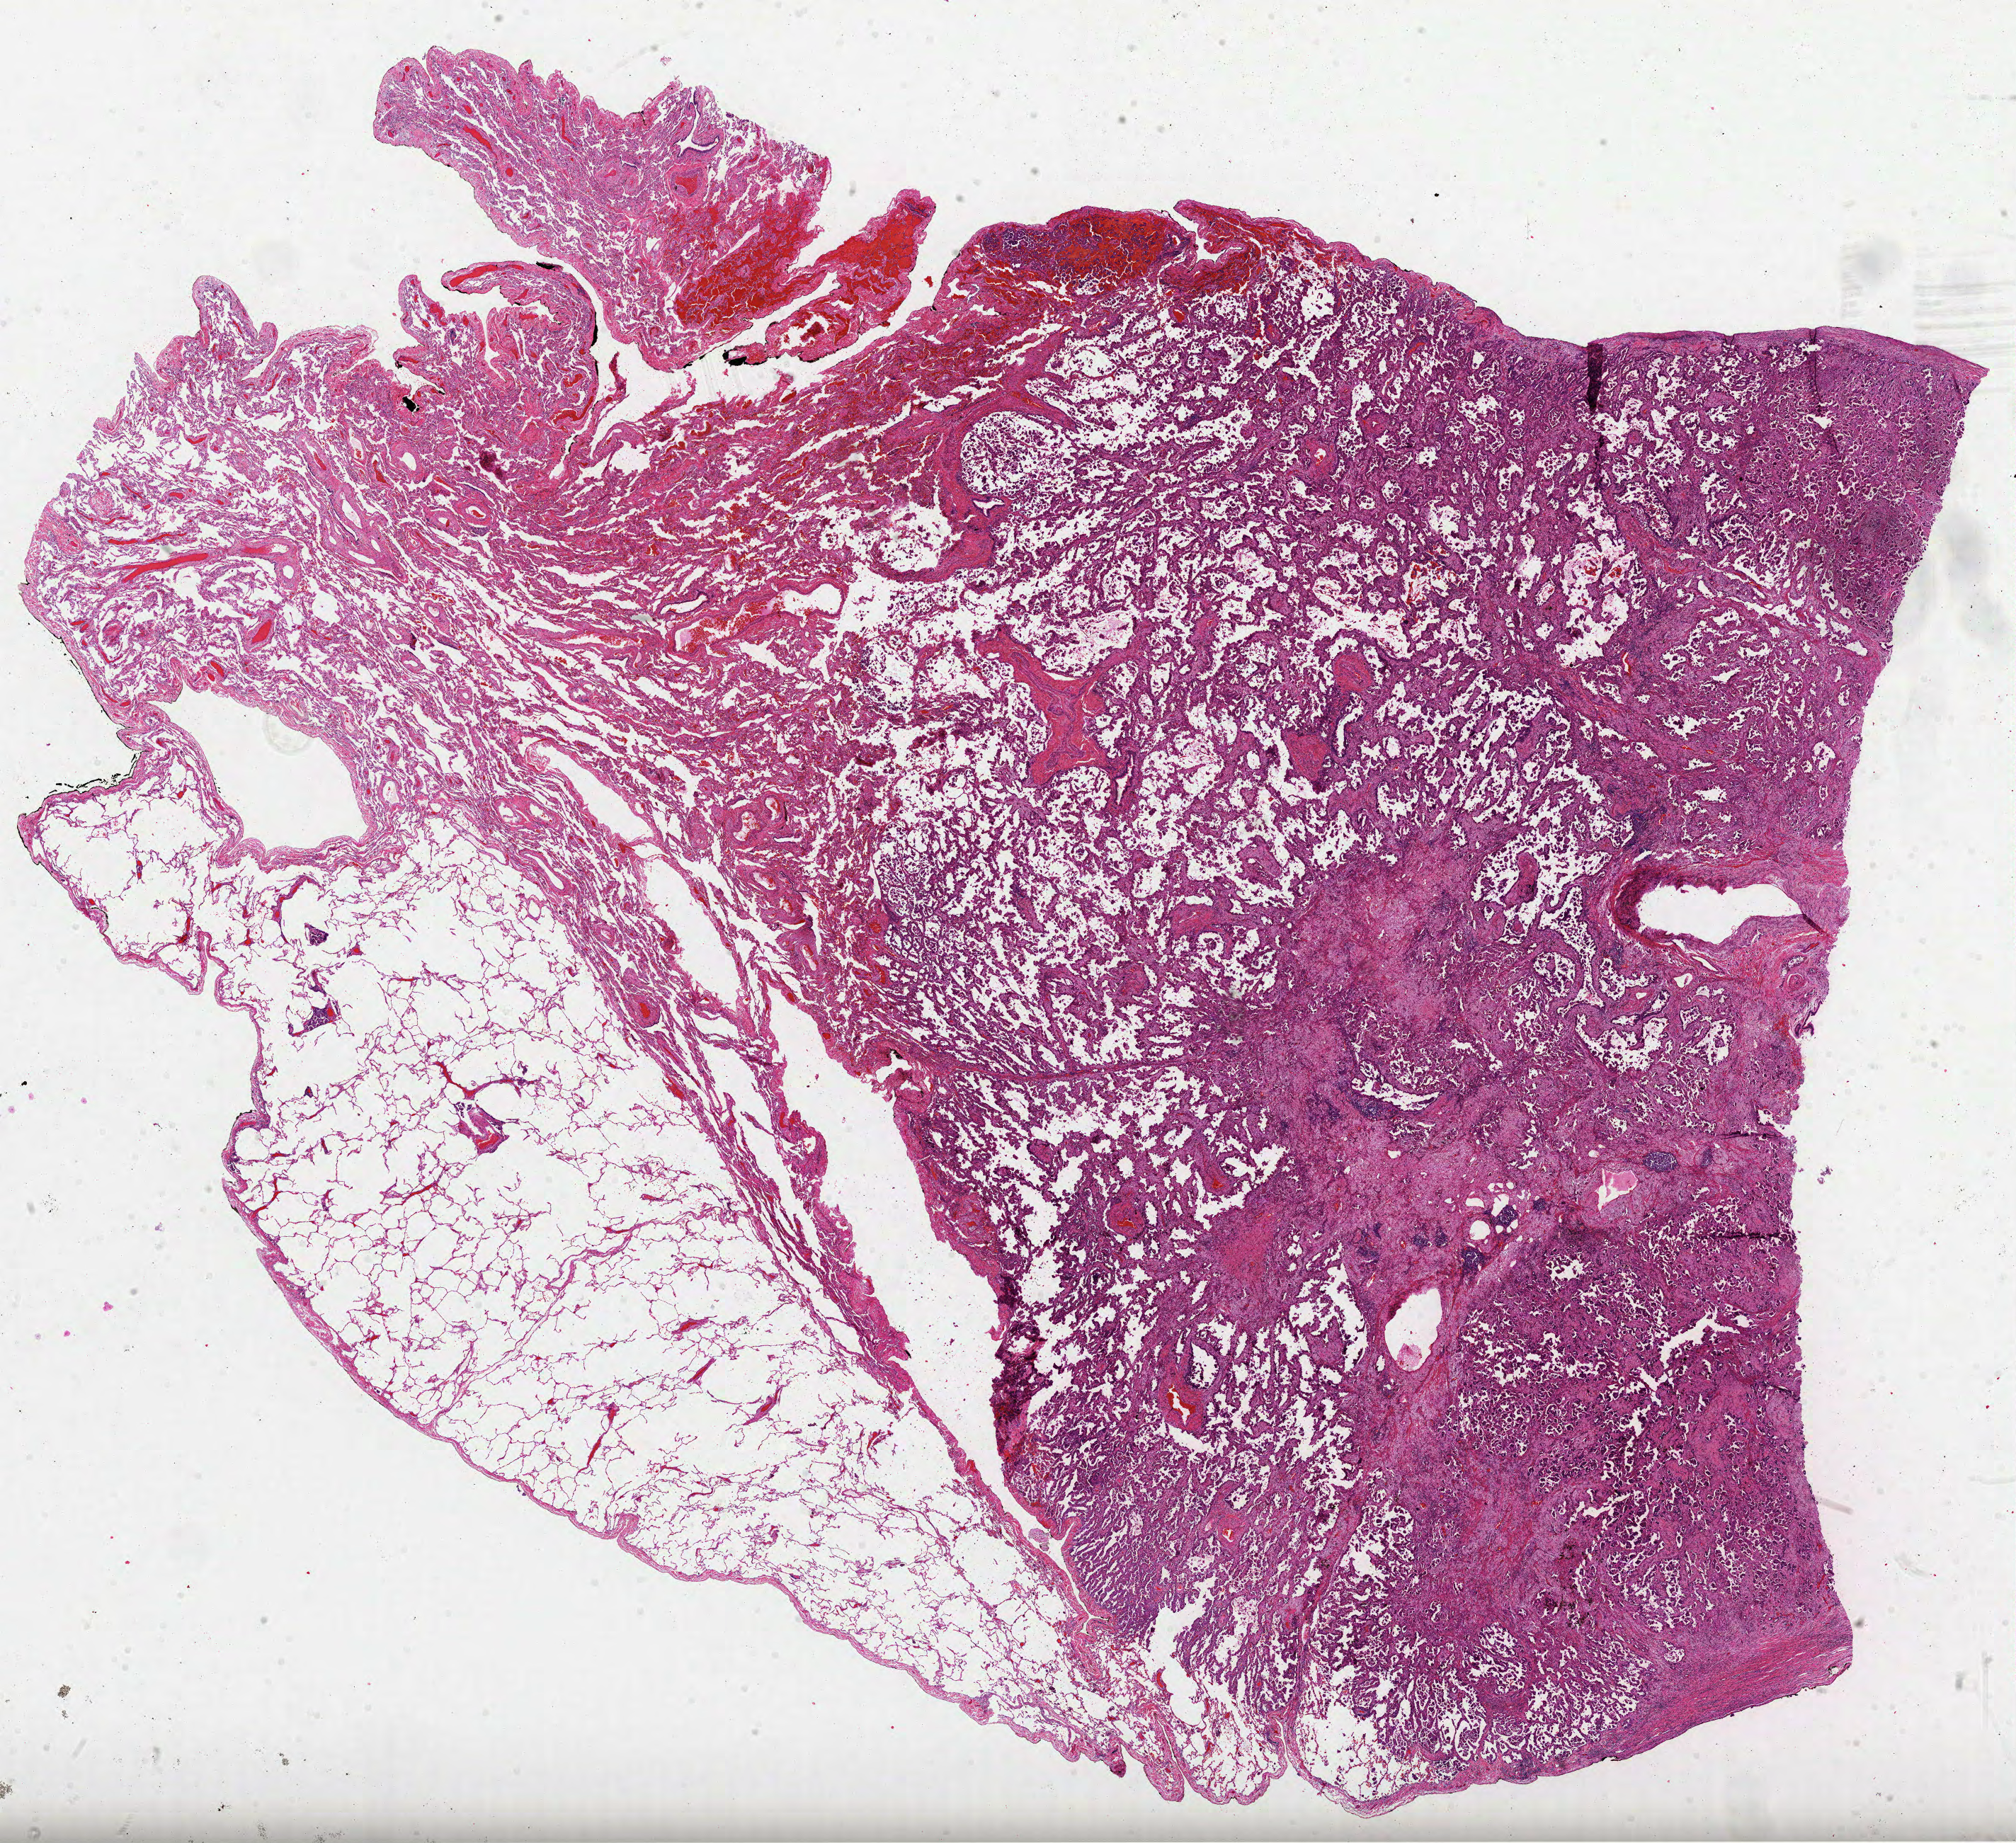
Whole-slide histology image, Hematoxylin and eosin (H&E) stained, whole scanned area (about 23.0 x 21.0 mm, acquisition: 40x scan) shown as a low-resolution overview. FFPE section. Primary tumour sample from the lung. Female patient; age at initial diagnosis 69 years.
* histologic diagnosis: Adenocarcinoma, NOS (middle lobe, lung)
* AJCC pathologic stage: IIIA (6th edition)